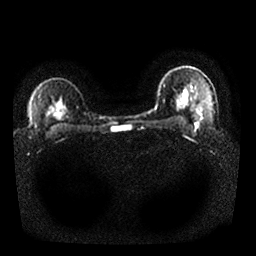
Breast MRI, one axial slice; position 19 of 25 along the scan axis; diffusion-weighted series; image 2 of 4 stored at this slice position (different b-values; order by instance number); 1.5 T; 4 mm slice thickness; 256 × 256 image matrix, field of view 340 × 340 mm. Female patient.
Structures marked on this image (outlined manually by an expert reader):
- tumour on diffusion-weighted imaging: box from (x=197, y=121) to (x=200, y=126) px